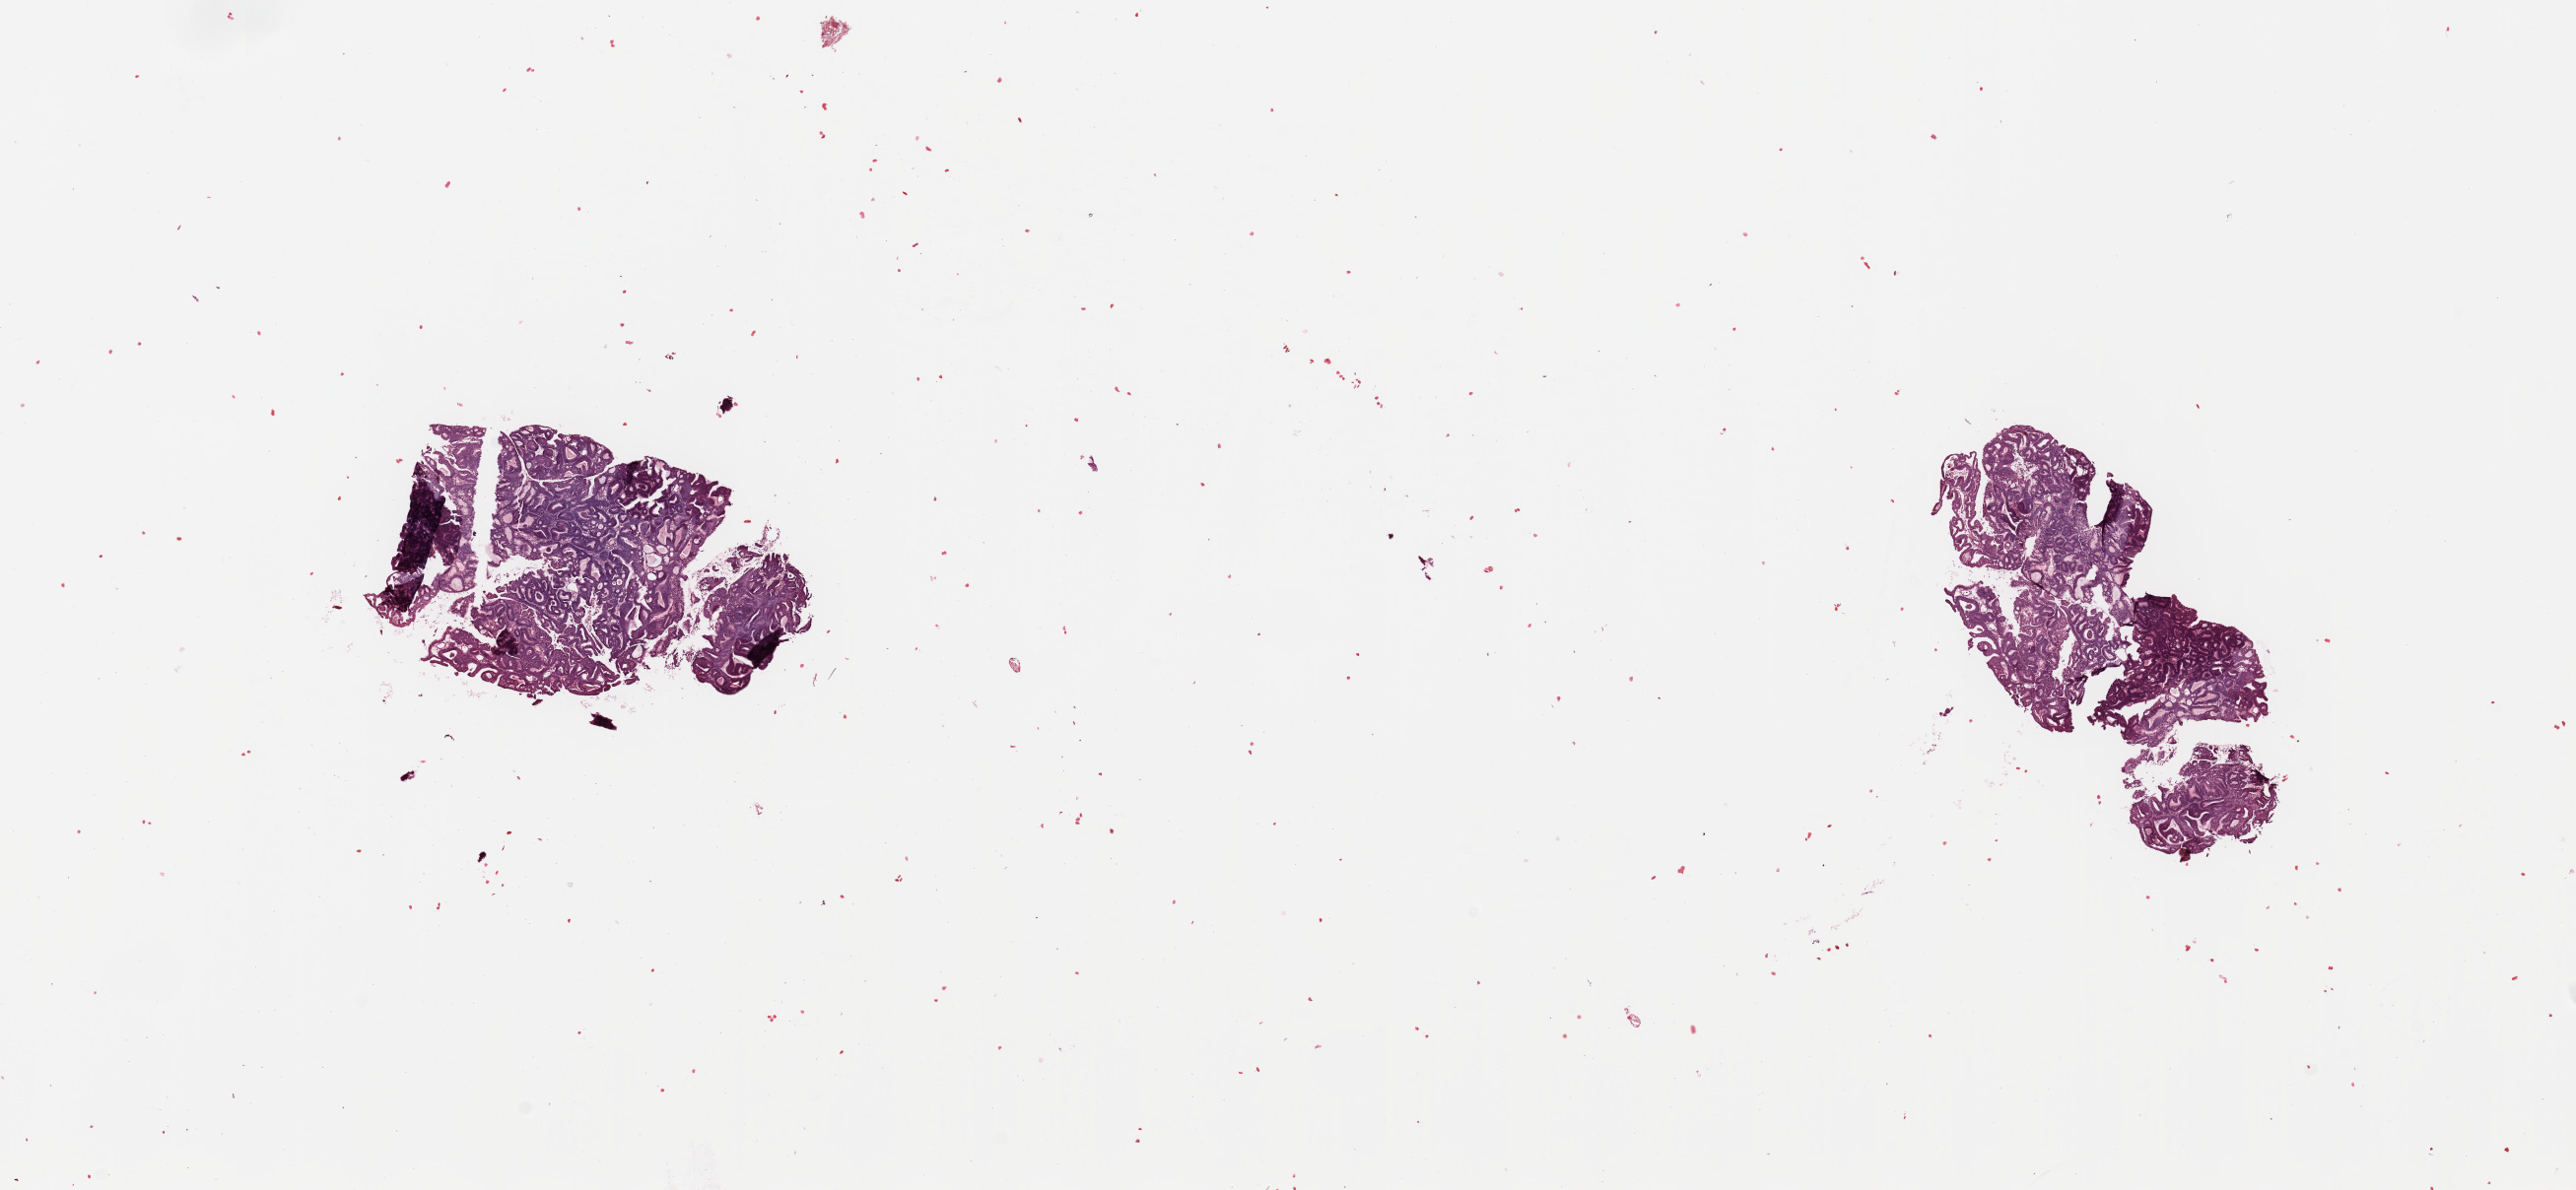
Digitized H&E tissue section (whole slide) — a low-resolution overview of the entire scanned area, about 20.7 x 9.6 mm (from a 20x scan), tumour tissue sample, uterus. Patient: female, age 57 years. Histologic grade: G2 (moderately differentiated).
AJCC pathologic stage: I. Primary tumour site (as recorded): anterior endometrium. Diagnosis: Endometrioid adenocarcinoma, NOS.